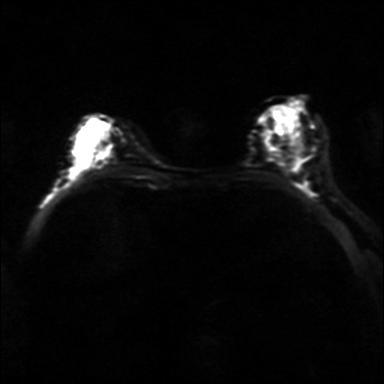
Breast MRI, one axial slice. Slice 19 of 36 in the series (ordered by position). Diffusion-weighted series; image 2 of 4 stored at this slice position (different b-values; order by instance number). 3 T. 4 mm slice thickness. 384 × 384 image matrix, field of view 320 × 320 mm. Female patient.
Annotated regions visible in this slice (manually delineated by an expert):
- tumour on diffusion-weighted imaging: bounding box [x1, y1, x2, y2] px = [101, 146, 115, 153]